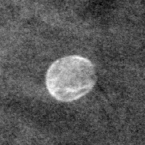
Cropped region of a digitized screen-film mammogram centred on a radiologist-marked abnormality; left breast; CC view.
Marked abnormality: calcifications, morphology lucent centered; BI-RADS assessment category 2; benign without callback (not worked up further).